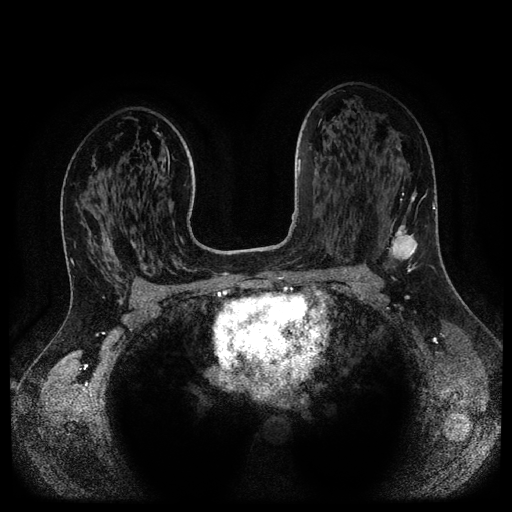
Breast MRI (dynamic contrast-enhanced, multi-phase), one axial slice. Position 66 of 116 along the scan axis. Dynamic contrast-enhanced series, time point 2 of 5 at this slice position (early post-contrast). 1.5 T. TE 2.6 ms, TR 5.3 ms. 2.1 mm slice thickness. 512 × 512 image matrix, field of view 360 × 360 mm. Female patient, age 37 years.
Outlined on this slice (semi-automatic segmentation, software-assisted and operator-edited):
- breast lesion (labelled 'tumour' in the annotation; benign lesions carry a separate 'benign' label): bounding box (x1, y1, x2, y2) in pixels: (388, 190, 427, 268)